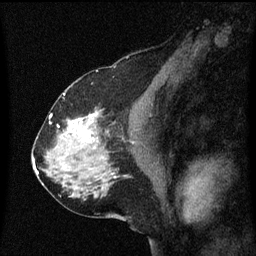
Breast MRI (dynamic contrast-enhanced), one sagittal slice; position 35 of 60 along the scan axis; dynamic contrast-enhanced series, image 2 of 3 at this slice position (ordered by acquisition); 1.5 T; TE 4.2 ms, TR 8.4 ms; 256 × 256 image matrix, field of view 200 × 200 mm. Female patient, age 58 years.
Structures marked on this image (semi-automatically segmented with operator editing):
- analysis volume of interest (the breast-tissue region the enhancement analysis was run in; not a lesion): bounding box [x1, y1, x2, y2] px = [58, 112, 99, 151]
- tumour enhancement mask (voxels above the 70 % enhancement threshold inside the analysis volume of interest): [62, 114, 99, 143]